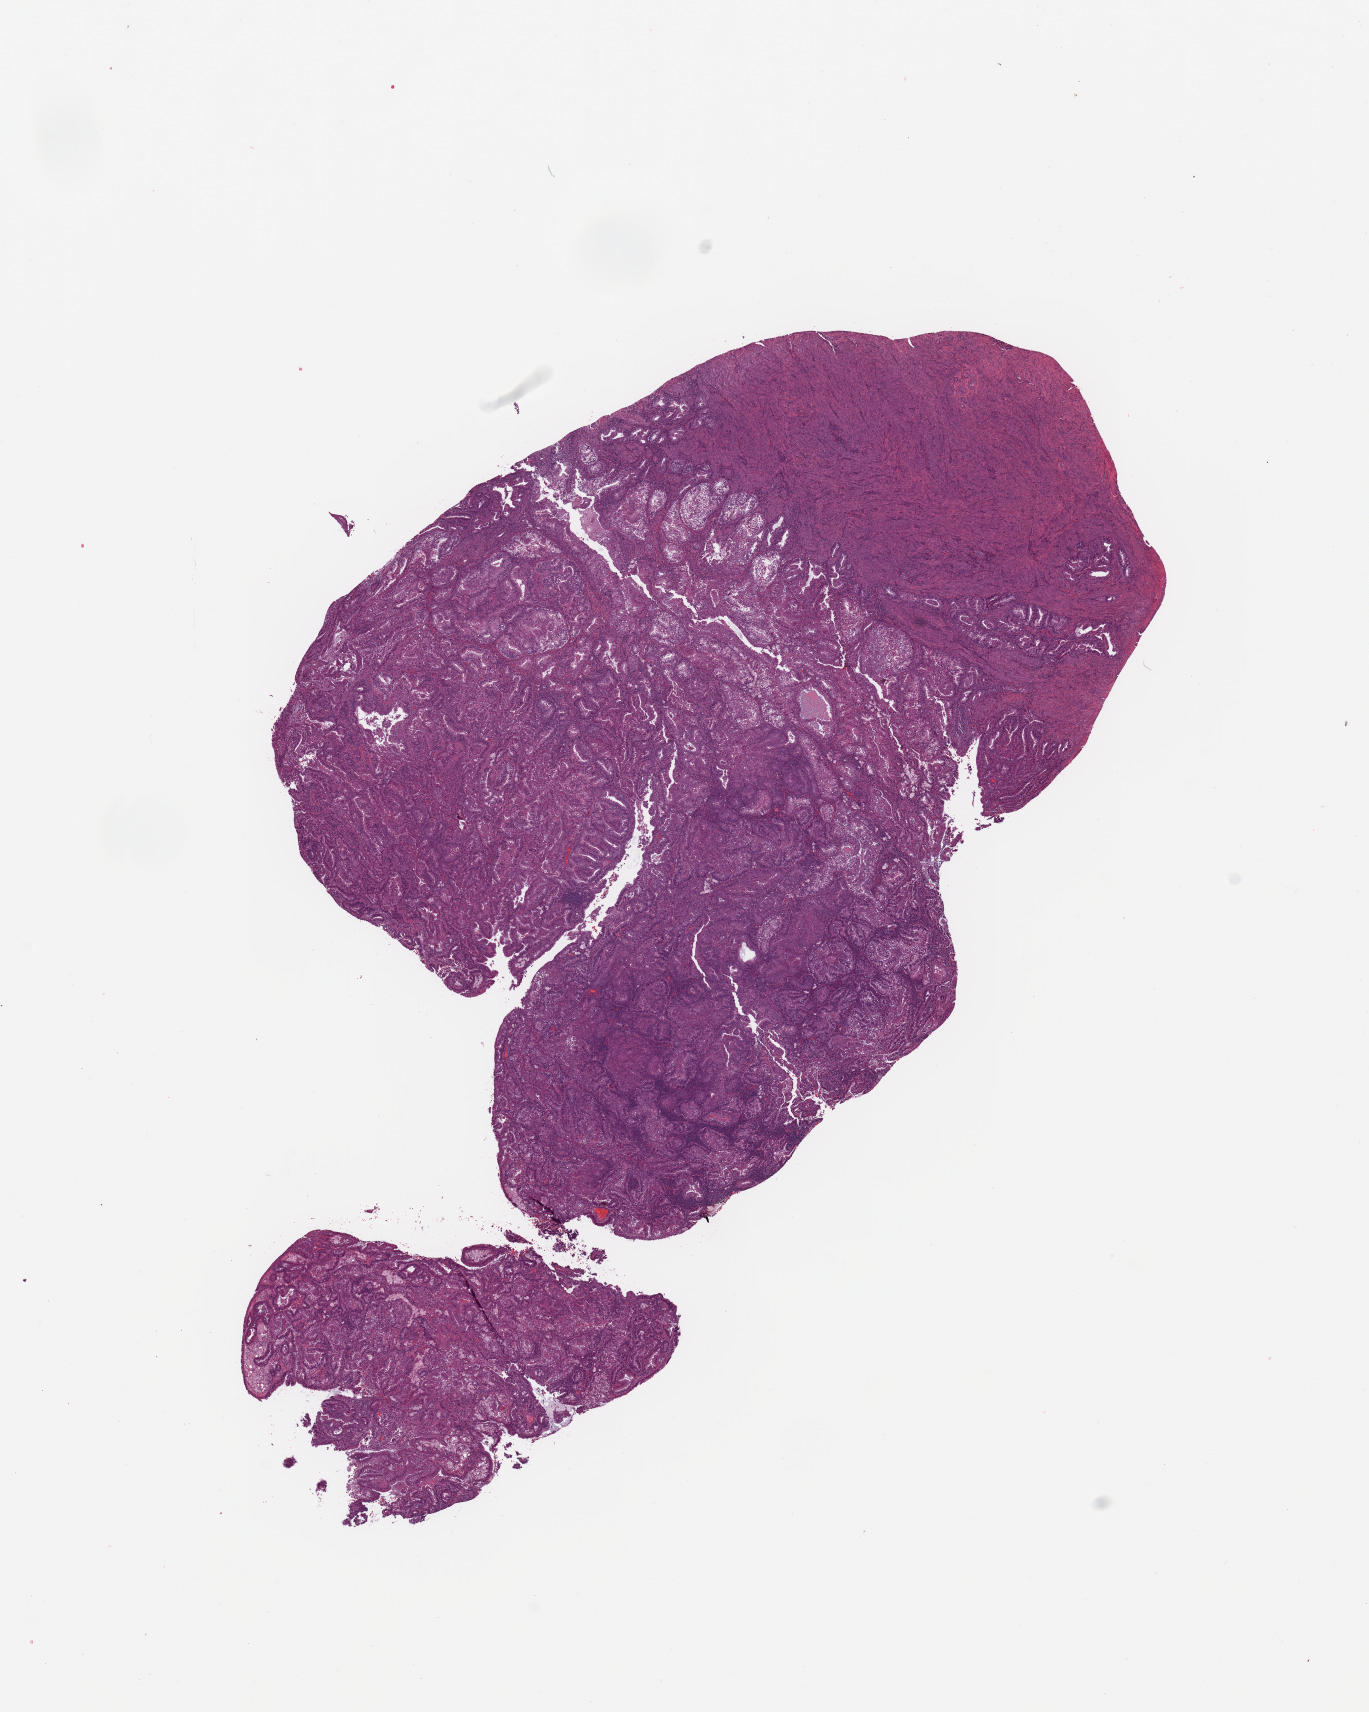
Hematoxylin and eosin (H&E) stained whole-slide image — whole scanned area (about 10.8 x 13.5 mm) shown as a low-resolution overview; tumour tissue sample, uterus. Female, 55 y/o. Histologic grade: G1 (well differentiated).
Diagnosis: Endometrioid adenocarcinoma, NOS. AJCC pathologic stage: I.